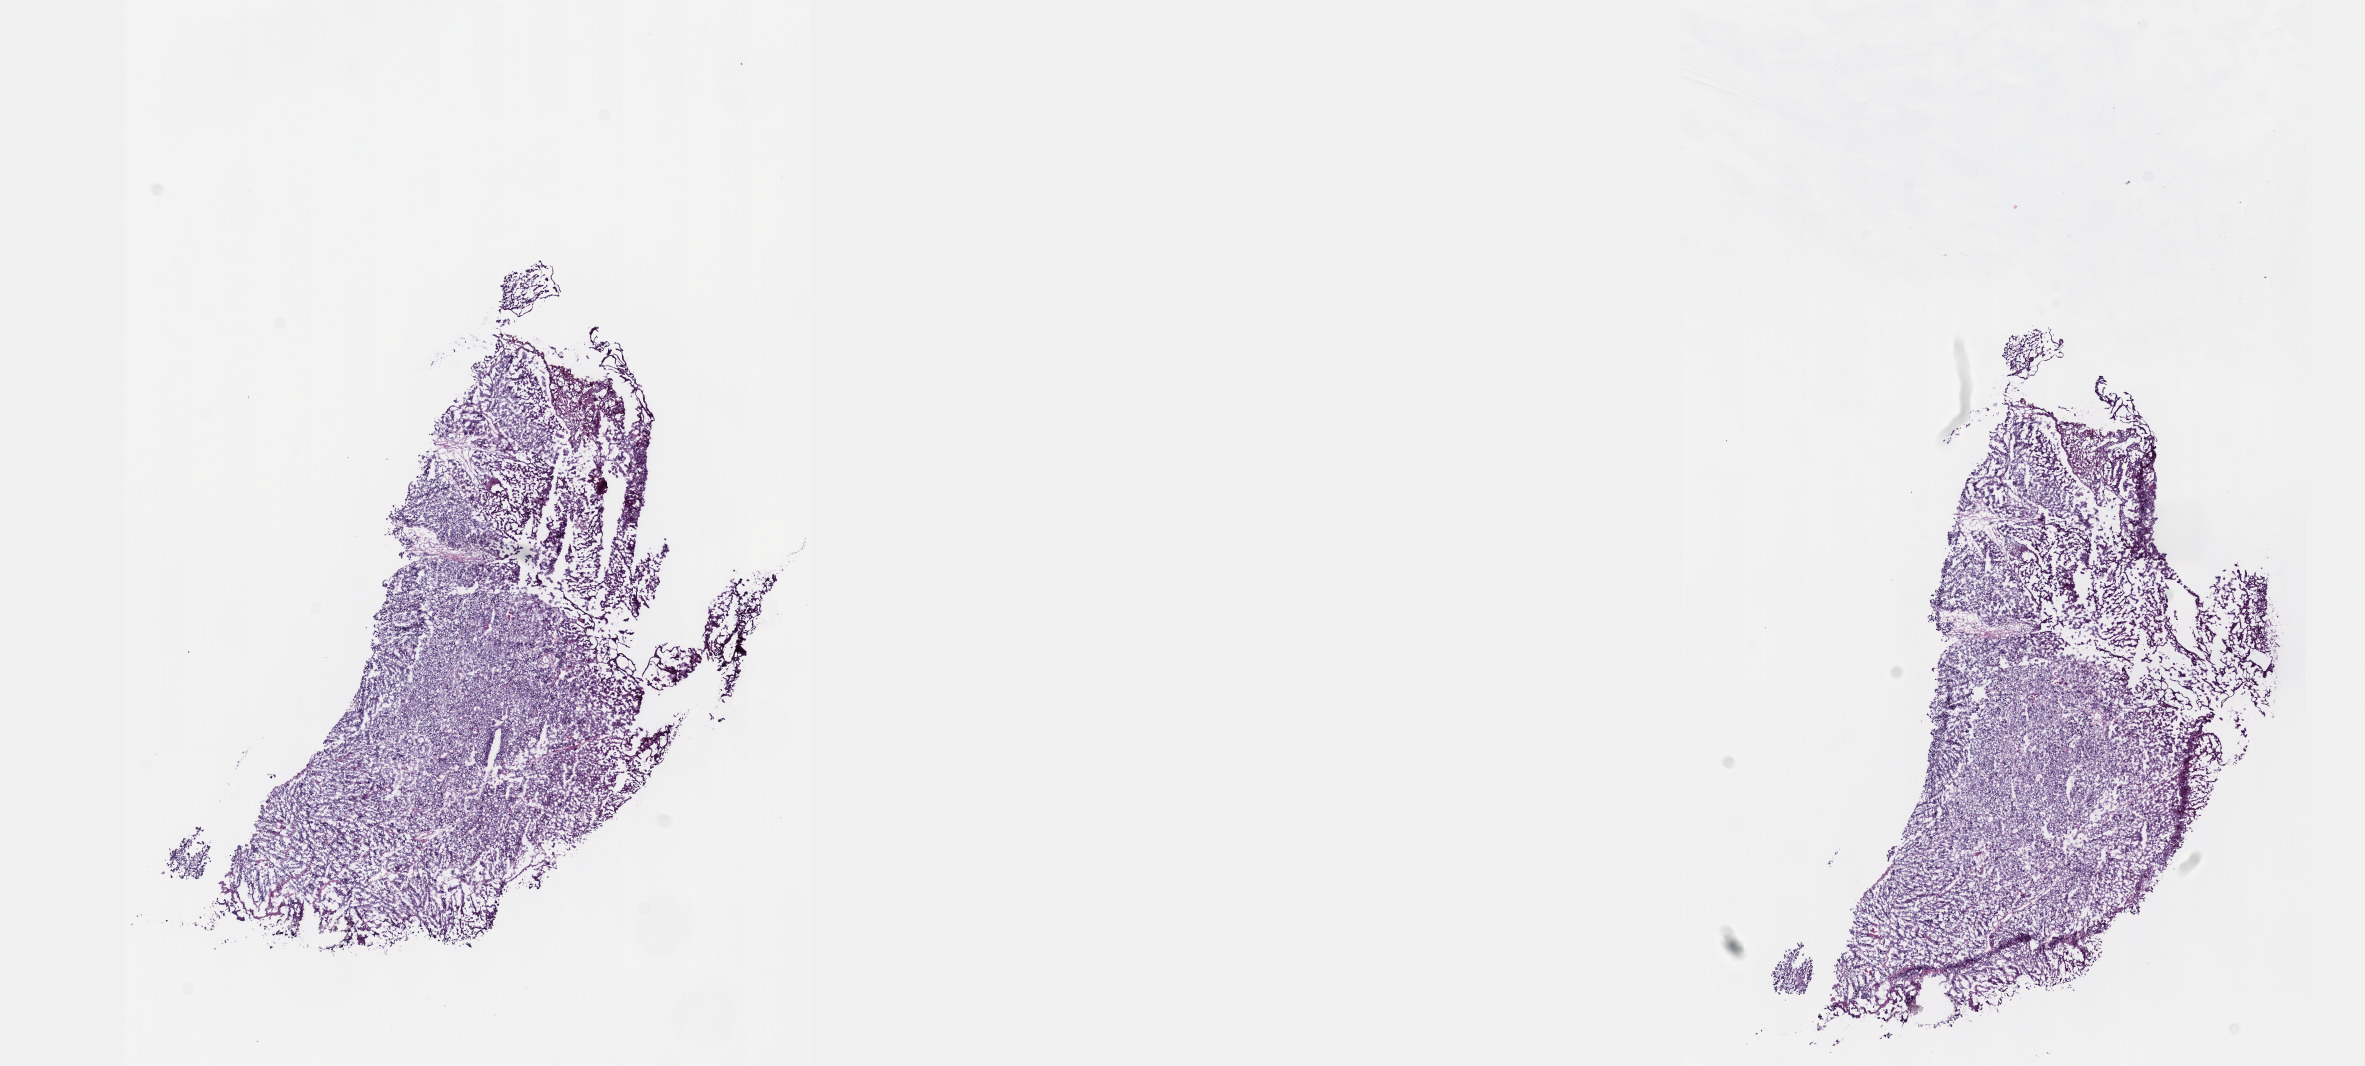
H&E whole-slide image — low-resolution overview of the scanned area, about 19.1 x 8.6 mm (acquisition: 40x scan); frozen section from the top of the tissue portion; primary tumour sample from the bladder. Male, age 70 years at initial diagnosis.
Histologic diagnosis: Transitional cell carcinoma.